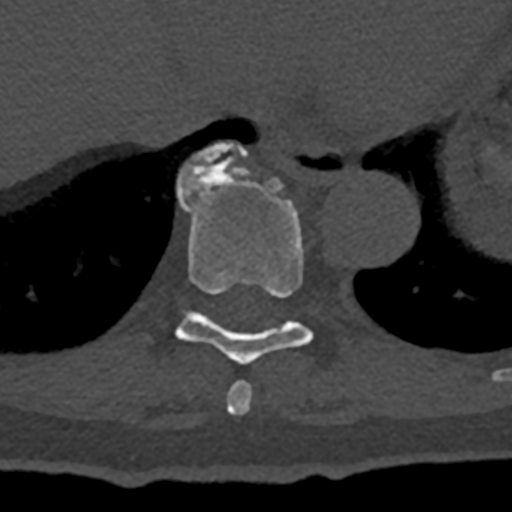
CT including the spine, one axial slice. Slice 651 of 797 in the series (ordered by position). Reconstruction kernel Br40s/3. 120 kVp. Bone window (W 1800 / L 400 HU). 0.5 mm slice thickness. 512 × 512 image matrix, field of view 160 × 160 mm. Male patient, age 74 years. From the clinical record (not read from this slice): primary cancer: renal; vertebrae with lytic lesions (as recorded): T10, L1, L2, L3, L4, L5.
Structures marked on this image (semi-automatically segmented with operator editing):
- T10 vertebra: bounding box [x1, y1, x2, y2] px = [177, 143, 248, 199]
- T8 vertebra: [227, 381, 252, 415]
- T9 vertebra: [175, 162, 313, 365]